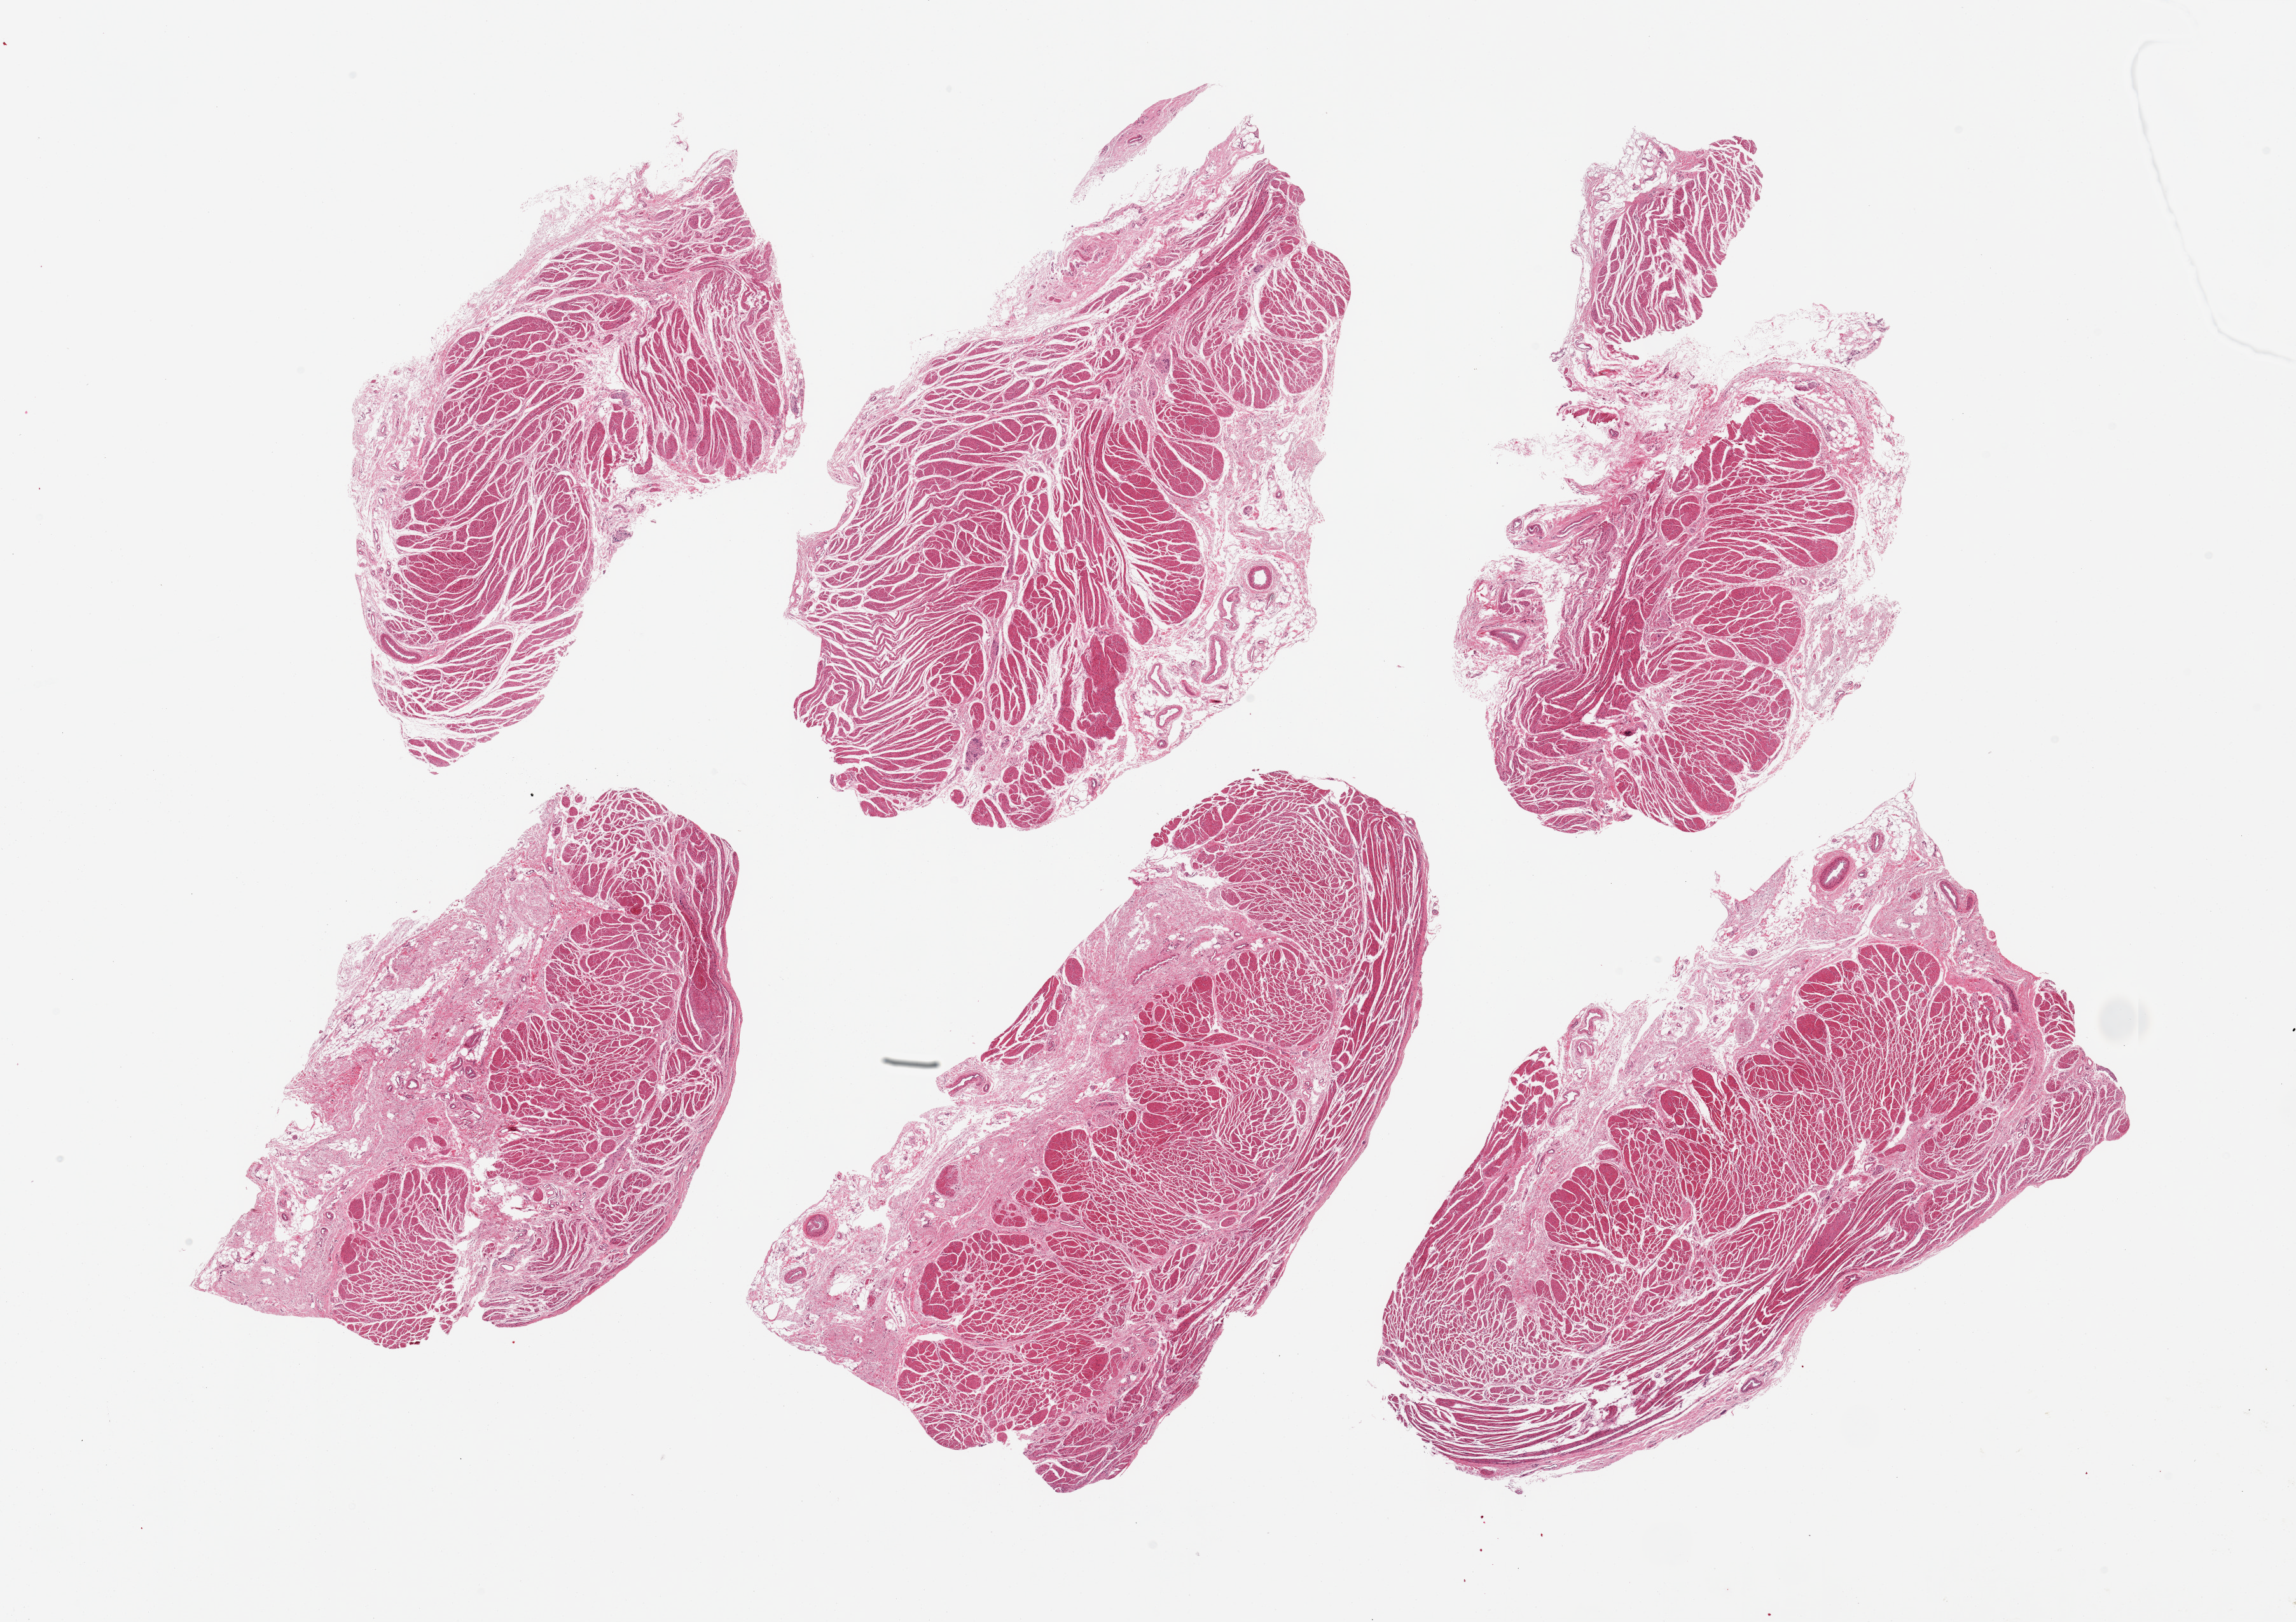
Digitized haematoxylin and eosin-stained section — shown as a low-resolution overview of the whole scanned area (about 28.5 x 20.2 mm, acquisition: 20x scan), PAXgene-fixed, paraffin-embedded tissue, sampled site (target tissue): gastroesophageal junction, donor tissue sample. Donor sex: female.
Pathologist's review note for this sample: 6 pieces with up to 30% submucosal fibrovascular stroma.